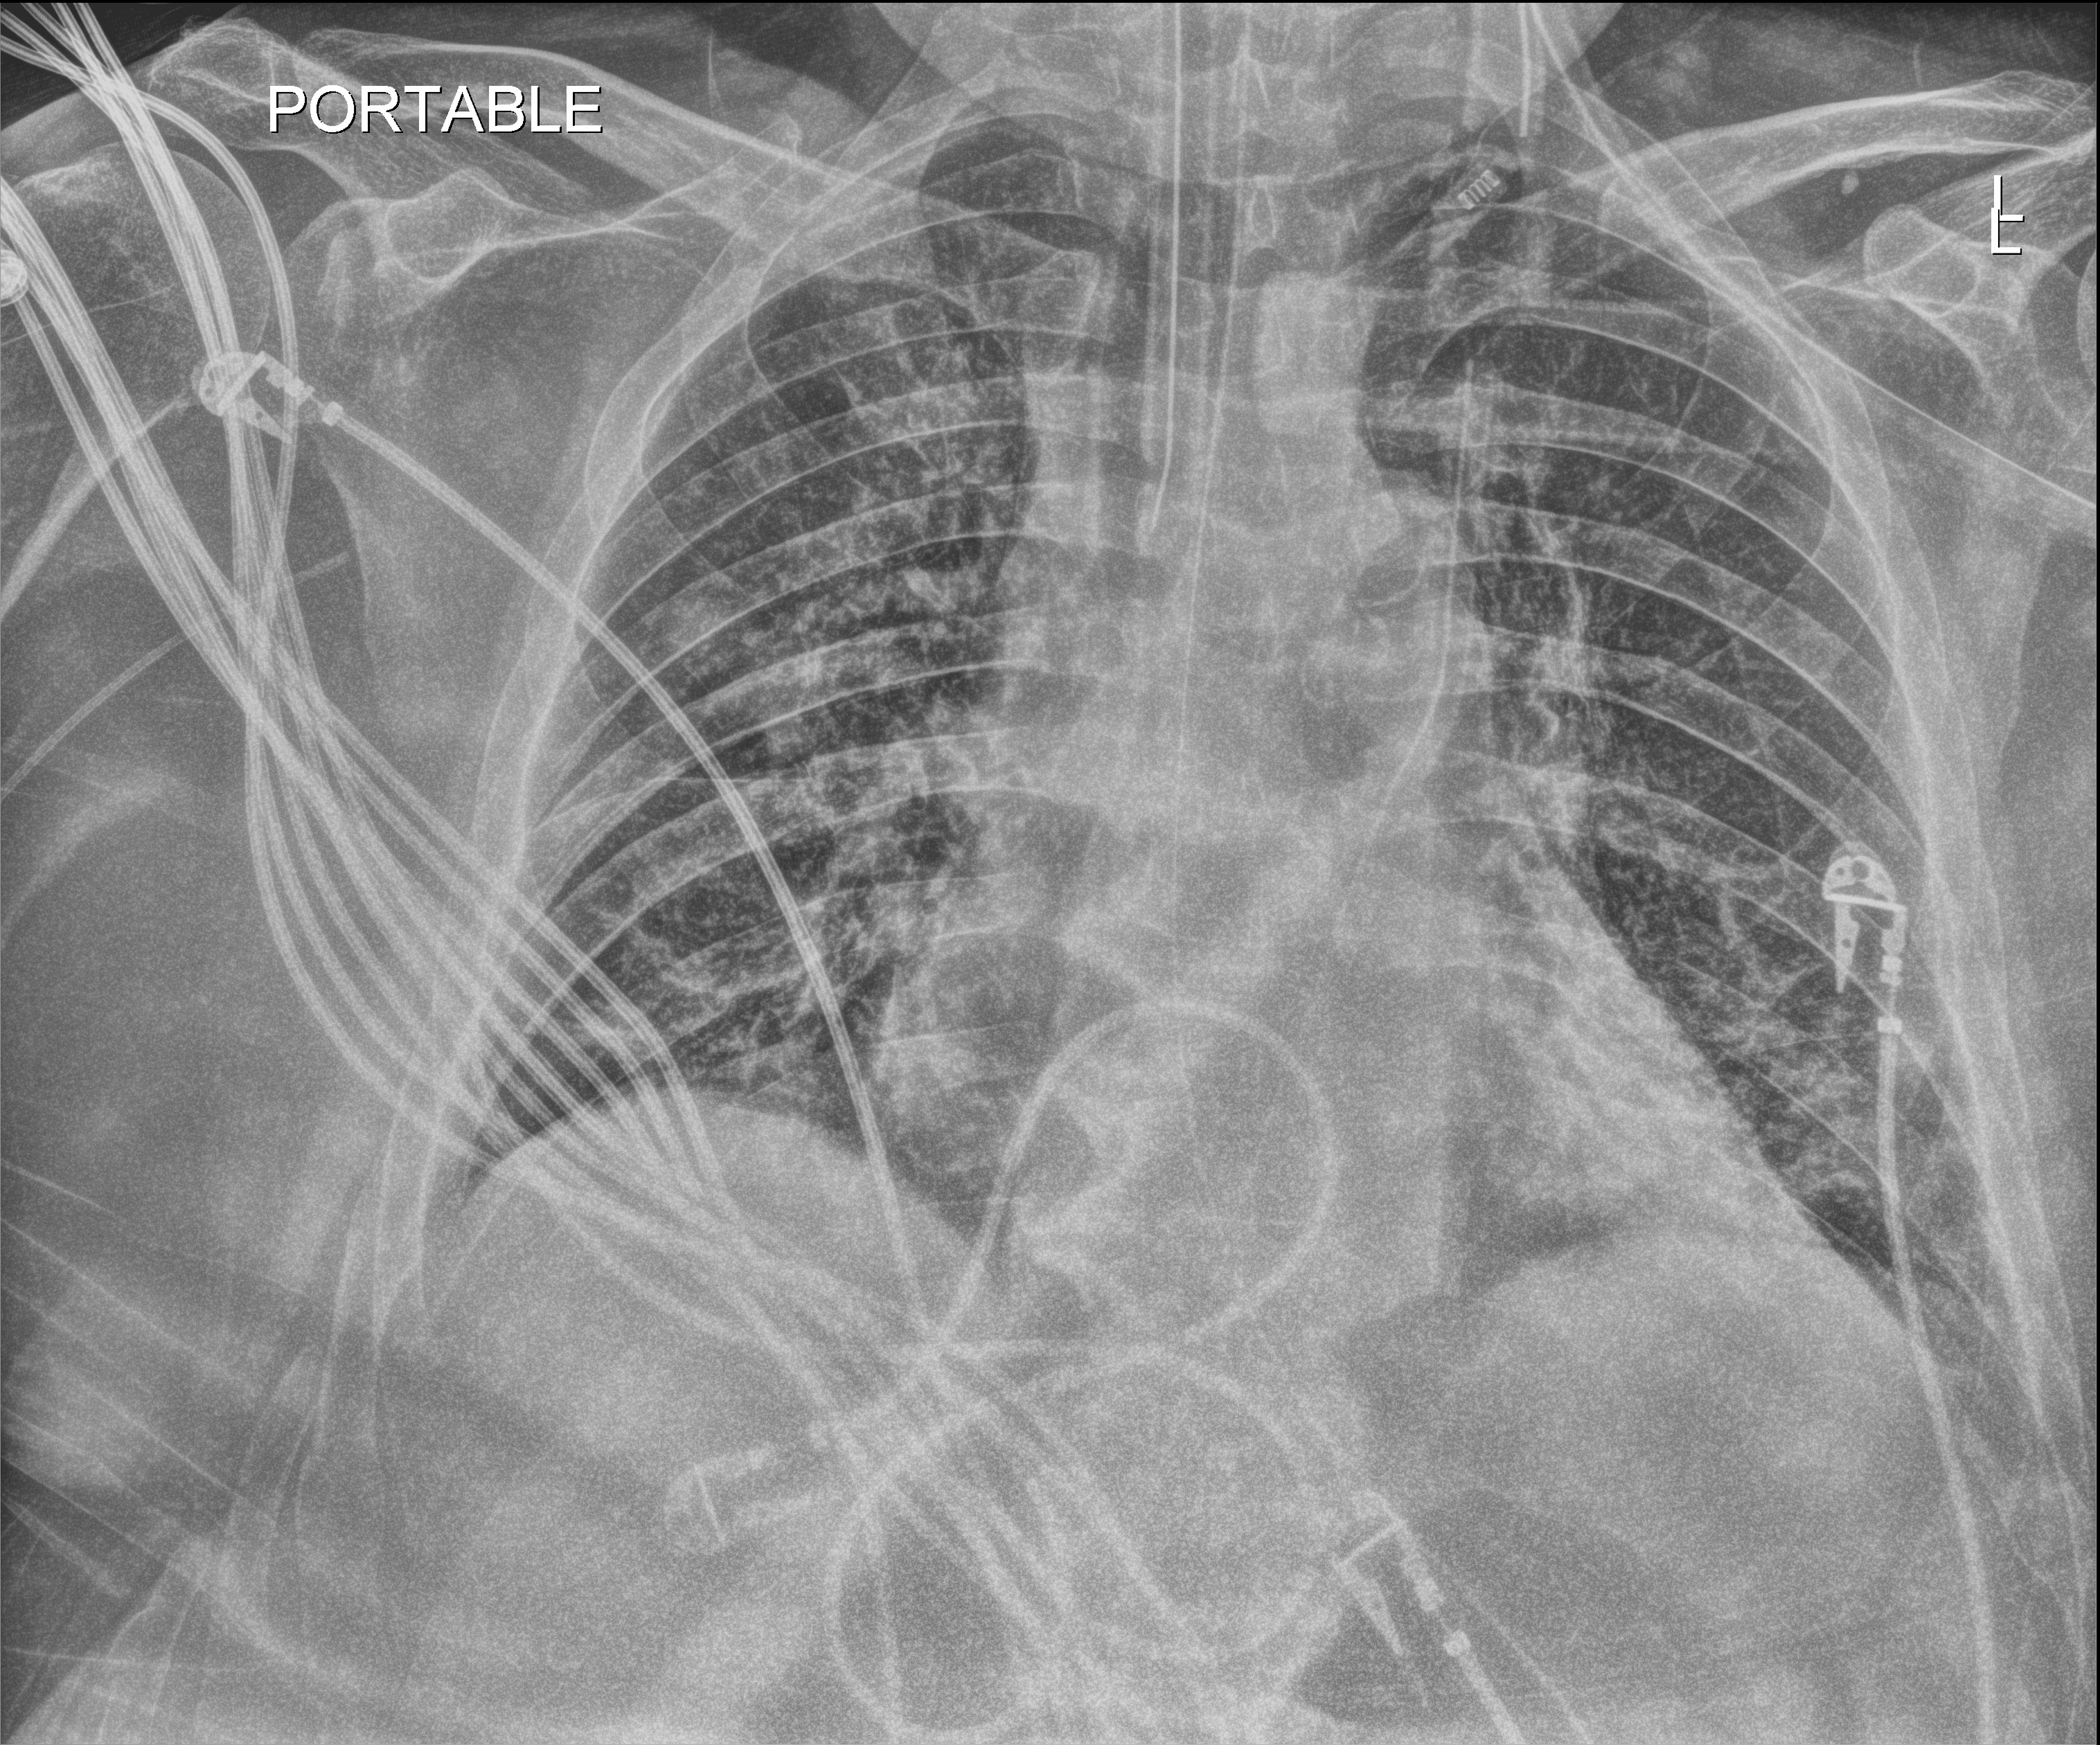
Portable chest radiograph. Patient hospitalised with COVID-19; male, aged 60–74 years.
Admission-level facts for this patient (not findings on this image; timing relative to this image not recorded): mechanically ventilated during this hospital stay: yes.